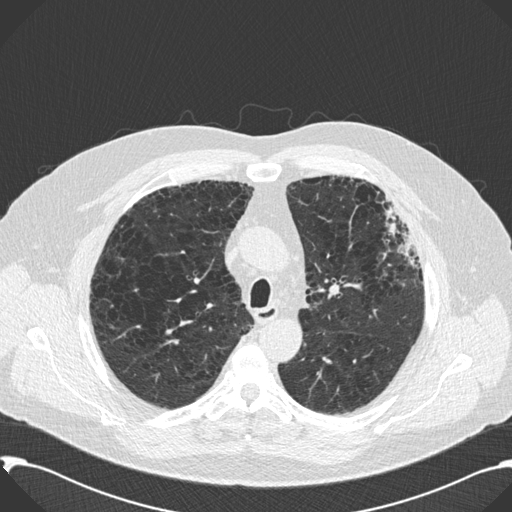
Low-dose screening chest CT, axial slice; second screening round (one year after baseline); lung window (W 1500 / L -600 HU); 2 mm slice thickness; 120 kVp; slice 51 of 199 in the series. Male, age 59 years at enrolment.
Expert-annotated lung lesion, bounding box [x1, y1, x2, y2] px = [362, 199, 425, 294]. Screening reader's record for this exam: no non-calcified nodule ≥4 mm recorded. Official screen result: negative screen, significant abnormalities not suspicious for lung cancer. Lung cancer was diagnosed 518 days after this screen: bronchiolo-alveolar carcinoma, mixed mucinous and non-mucinous, left upper lobe, stage IA (AJCC 6th edition), 20 mm at pathology.